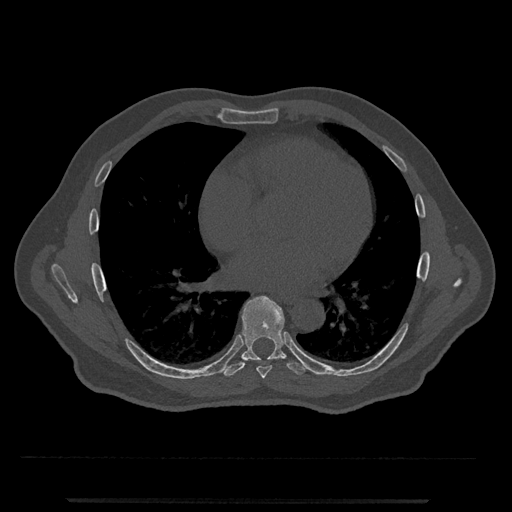
CT including the spine, one axial slice. Slice 650 of 797 in the series (ordered by position). 120 kVp. Bone window (W 1800 / L 400 HU). 512 × 512 image matrix, field of view 419 × 419 mm. Patient: male, 63 years. From the clinical record (not read from this slice): primary cancer: prostate.
Structures marked on this image (semi-automatic segmentation, software-assisted and operator-edited):
- T7 vertebra: bounding box <257,366,272,379> (left, top, right, bottom; pixels)
- T8 vertebra: <223,296,307,377>